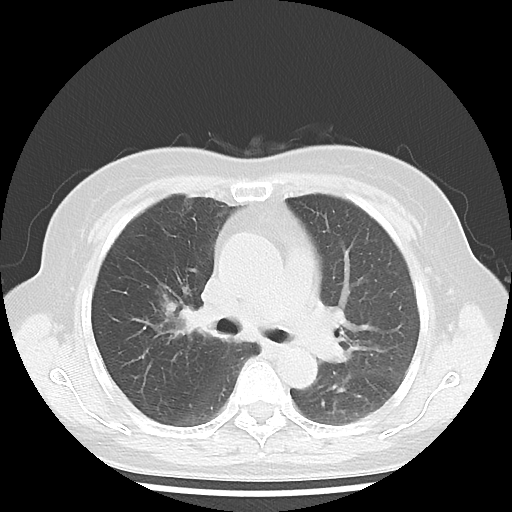
Chest CT, one axial slice. Position 25 of 43 along the scan axis. Reconstruction kernel LUNG. Lung window (W 1500 / L -600 HU). 512 × 512 image matrix. Female patient, age 62 years. From the clinical record (not read from this slice): clinical TNM (as recorded): T3 N0 M0; histopathological grade: G3.
Annotated regions visible in this slice (rectangle marked by the reading radiologist):
- lung tumour (recorded histology: small cell carcinoma): bounding box <148,285,213,359> (left, top, right, bottom; pixels)